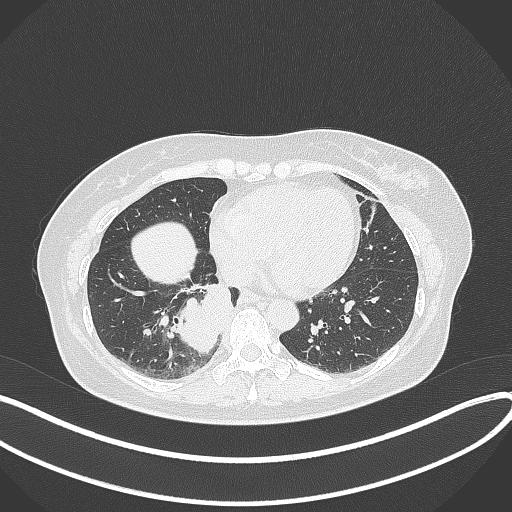
Chest CT, one axial slice. Position 120 of 331 along the scan axis. Reconstruction kernel B70f. 120 kVp. Lung window (W 1500 / L -600 HU). 1 mm slice thickness. 512 × 512 image matrix. Female patient, age 54 years. From the clinical record (not read from this slice): clinical TNM (as recorded): T4 N0 M0.
Outlined on this slice (rectangle marked by the reading radiologist):
- lung tumour (recorded histology: adenocarcinoma): bounding box [x1, y1, x2, y2] px = [165, 272, 240, 361]